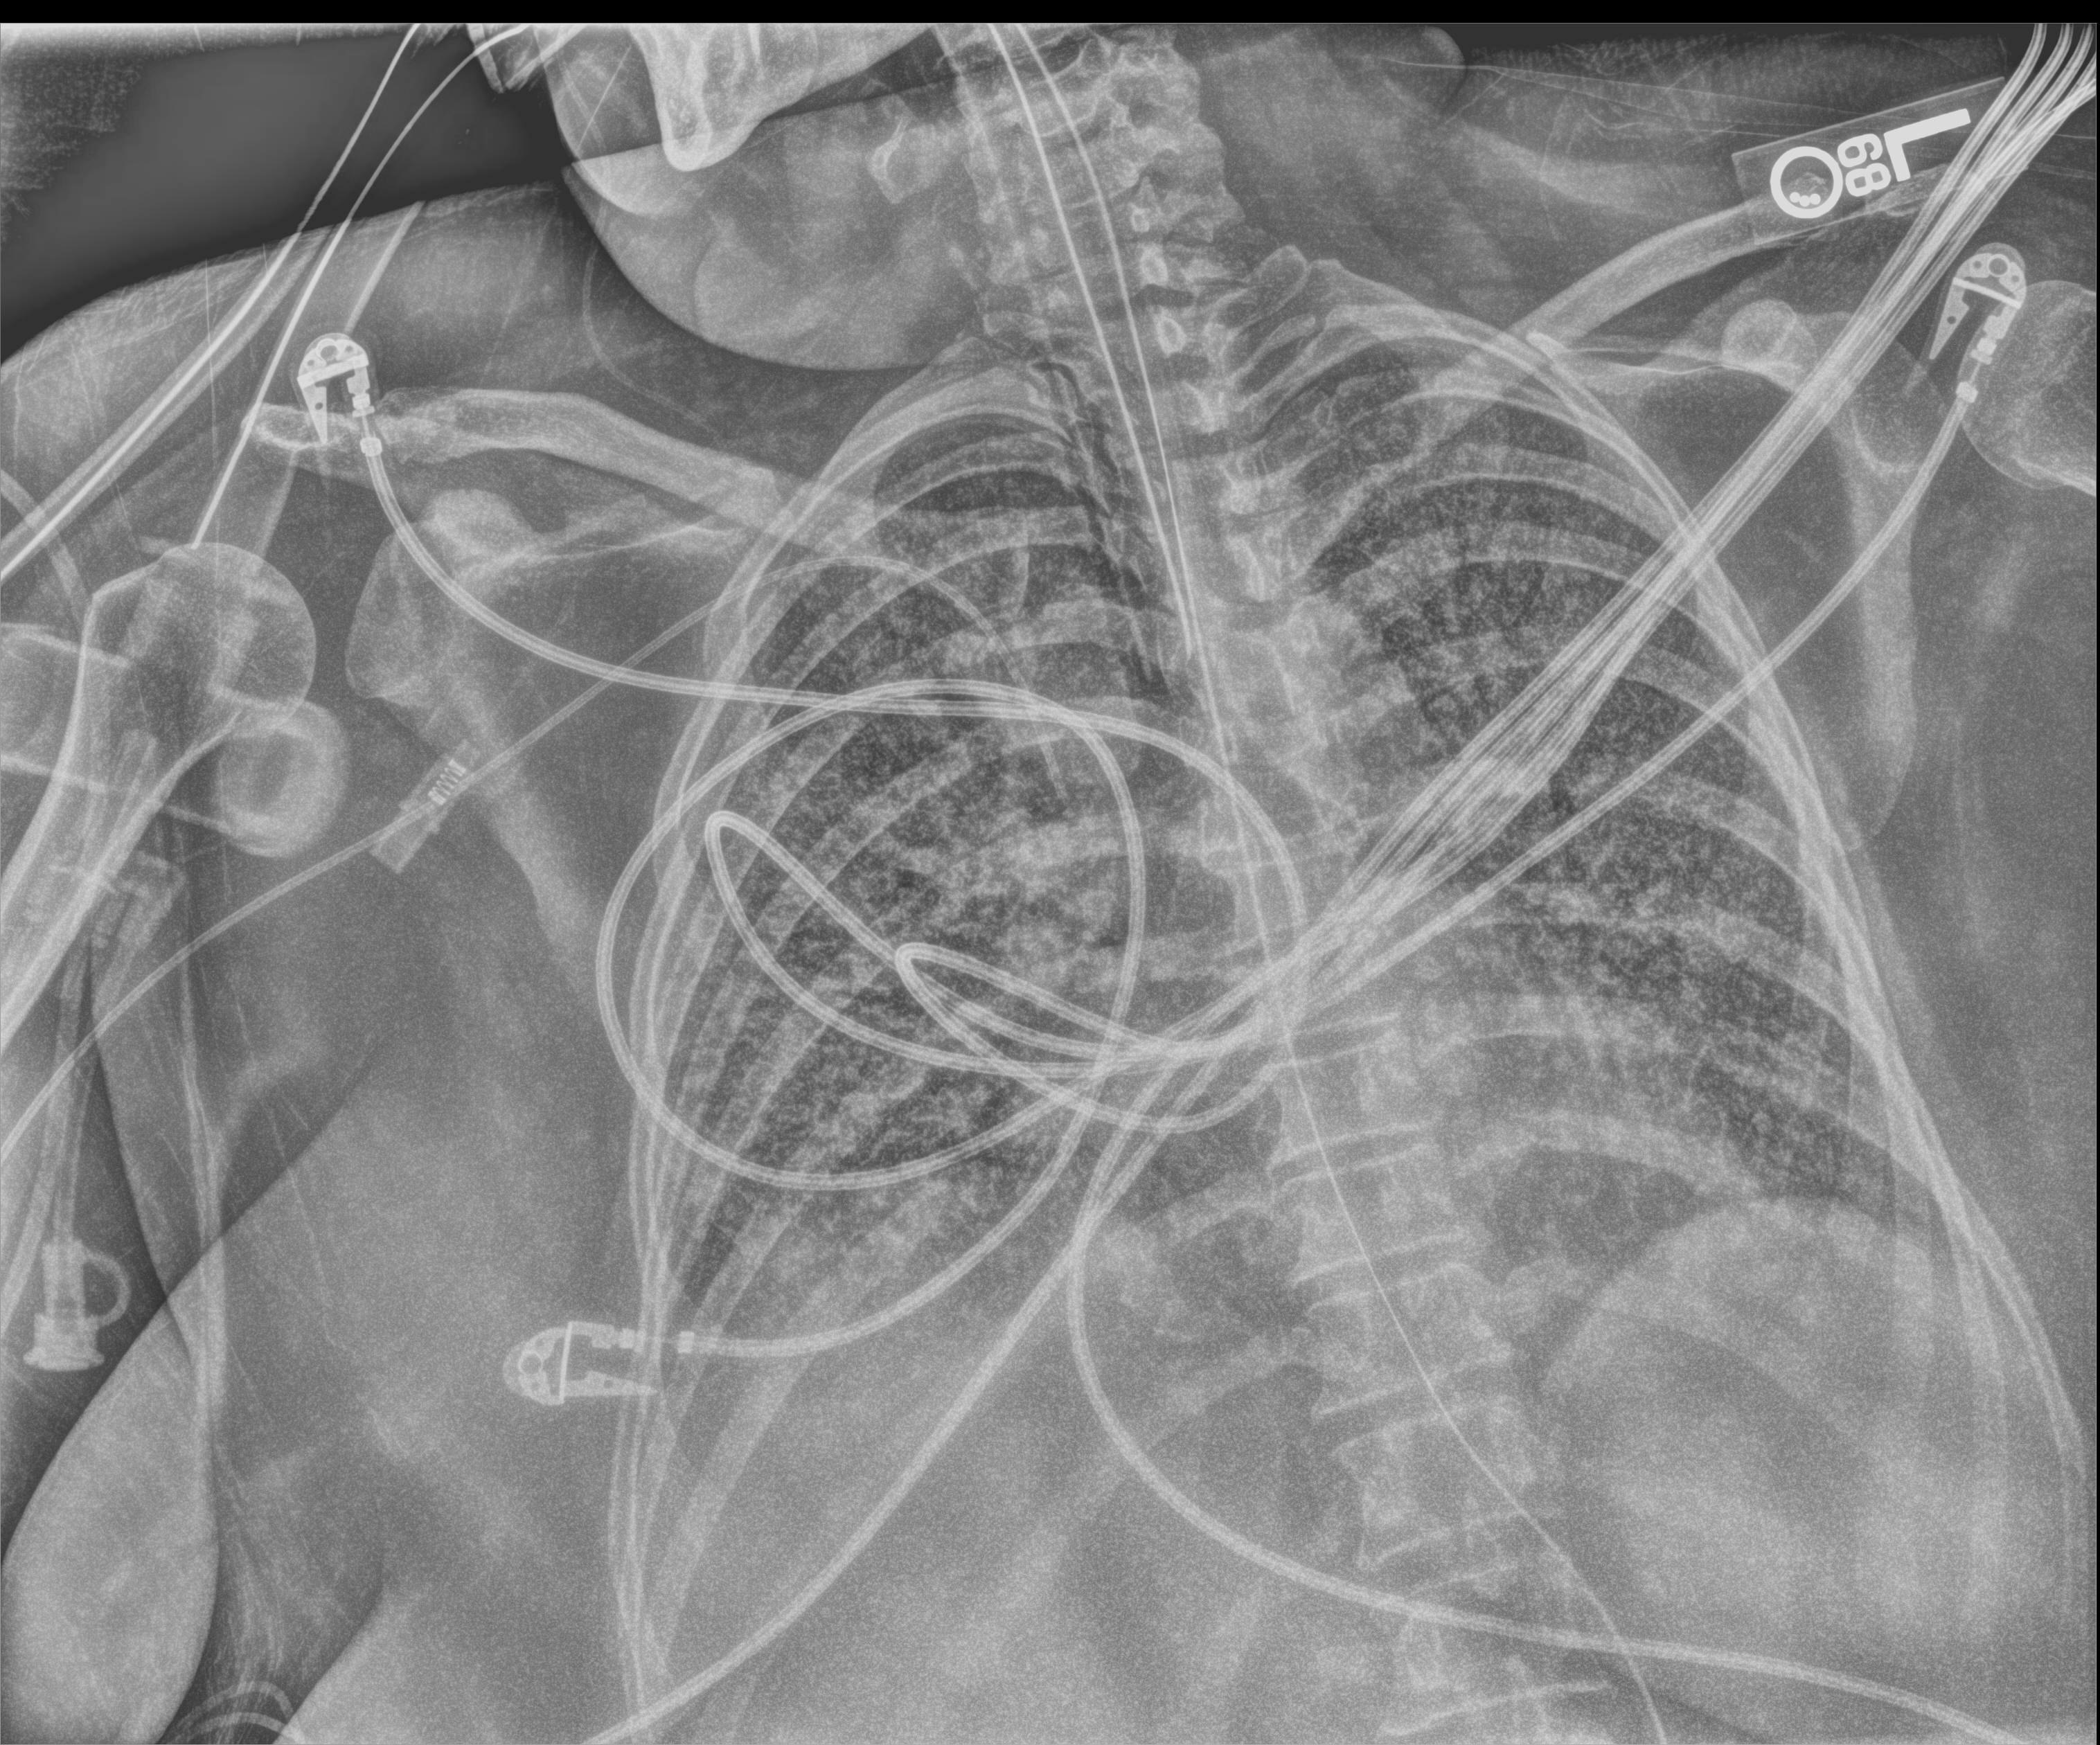
Chest X-ray (portable), anteroposterior (AP) projection. Patient hospitalised with COVID-19; female, aged 18–59 years.
Hospital-stay facts (about this admission, not read from this image; timing relative to this image not recorded): chronic kidney disease (admission record): no; mechanically ventilated during this hospital stay: yes.